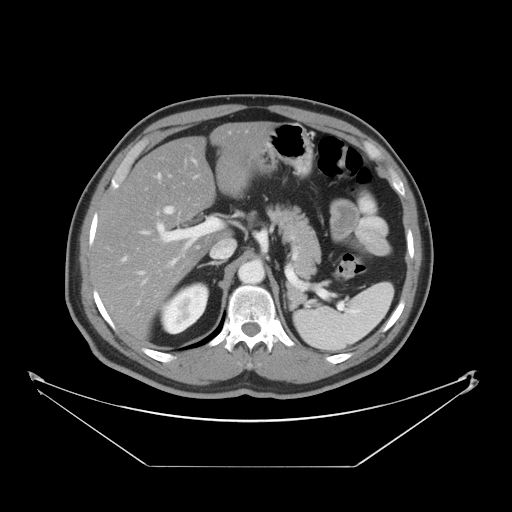
Contrast-enhanced abdominal CT, one axial slice; reconstruction kernel STANDARD; 120 kVp; intravenous contrast given; soft-tissue window (W 400 / L 40 HU); 512 × 512 image matrix. Male patient, age 57 years. Case-level facts recorded for this patient, not image findings: diagnosis: colorectal cancer liver metastases, imaged before liver resection; multiple liver metastases: no; largest metastasis: 3.3 cm.
Outlined on this slice (outlined manually by an expert reader):
- hepatic veins: bounding box (x1, y1, x2, y2) in pixels: (157, 177, 175, 214)
- liver: (94, 123, 265, 340)
- planned liver remnant (the part of the liver to remain after resection): (94, 123, 265, 339)
- portal vein (with intrahepatic branches): (139, 217, 222, 272)